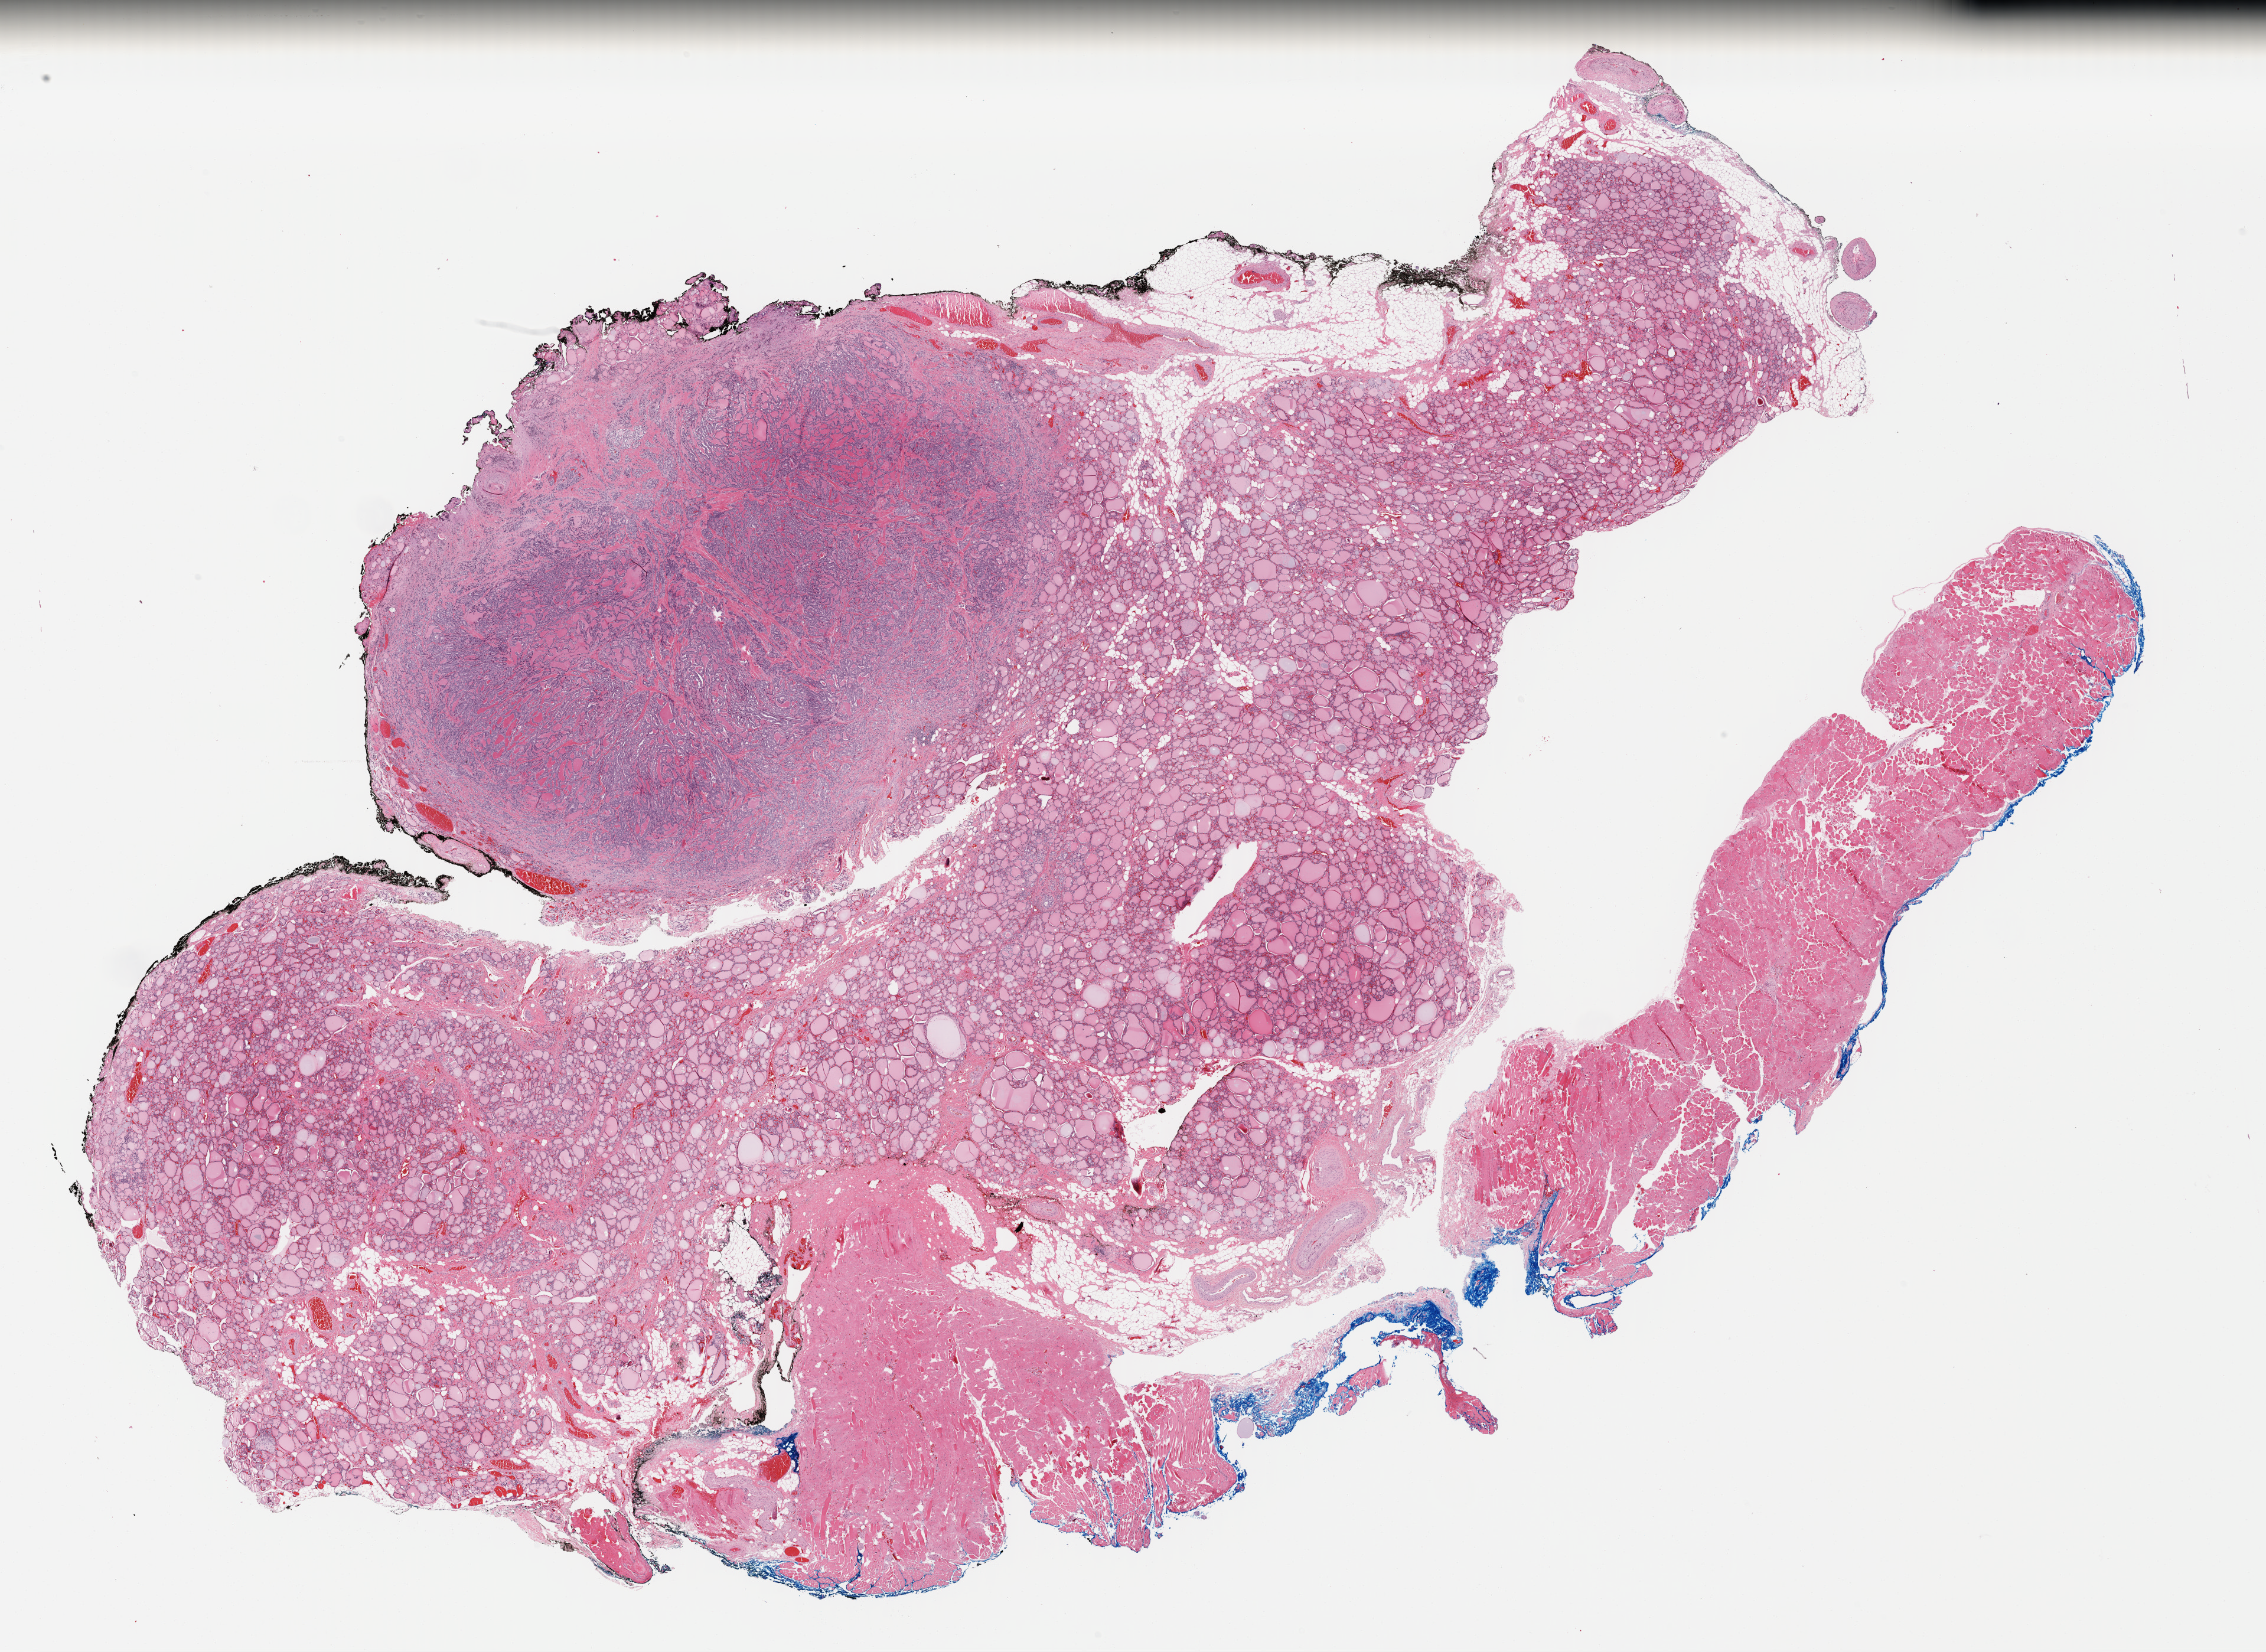
Hematoxylin and eosin (H&E) stained whole-slide image — whole scanned area (about 30.2 x 22.0 mm) shown as a low-resolution overview; FFPE section; sample: primary tumour, thyroid. Female patient; age at initial diagnosis 68 years.
- laterality: left
- lymph nodes positive (case pathology): 0 of 3 examined
- diagnosis: Papillary adenocarcinoma, NOS (thyroid gland)
- AJCC pathologic stage: I (7th edition)